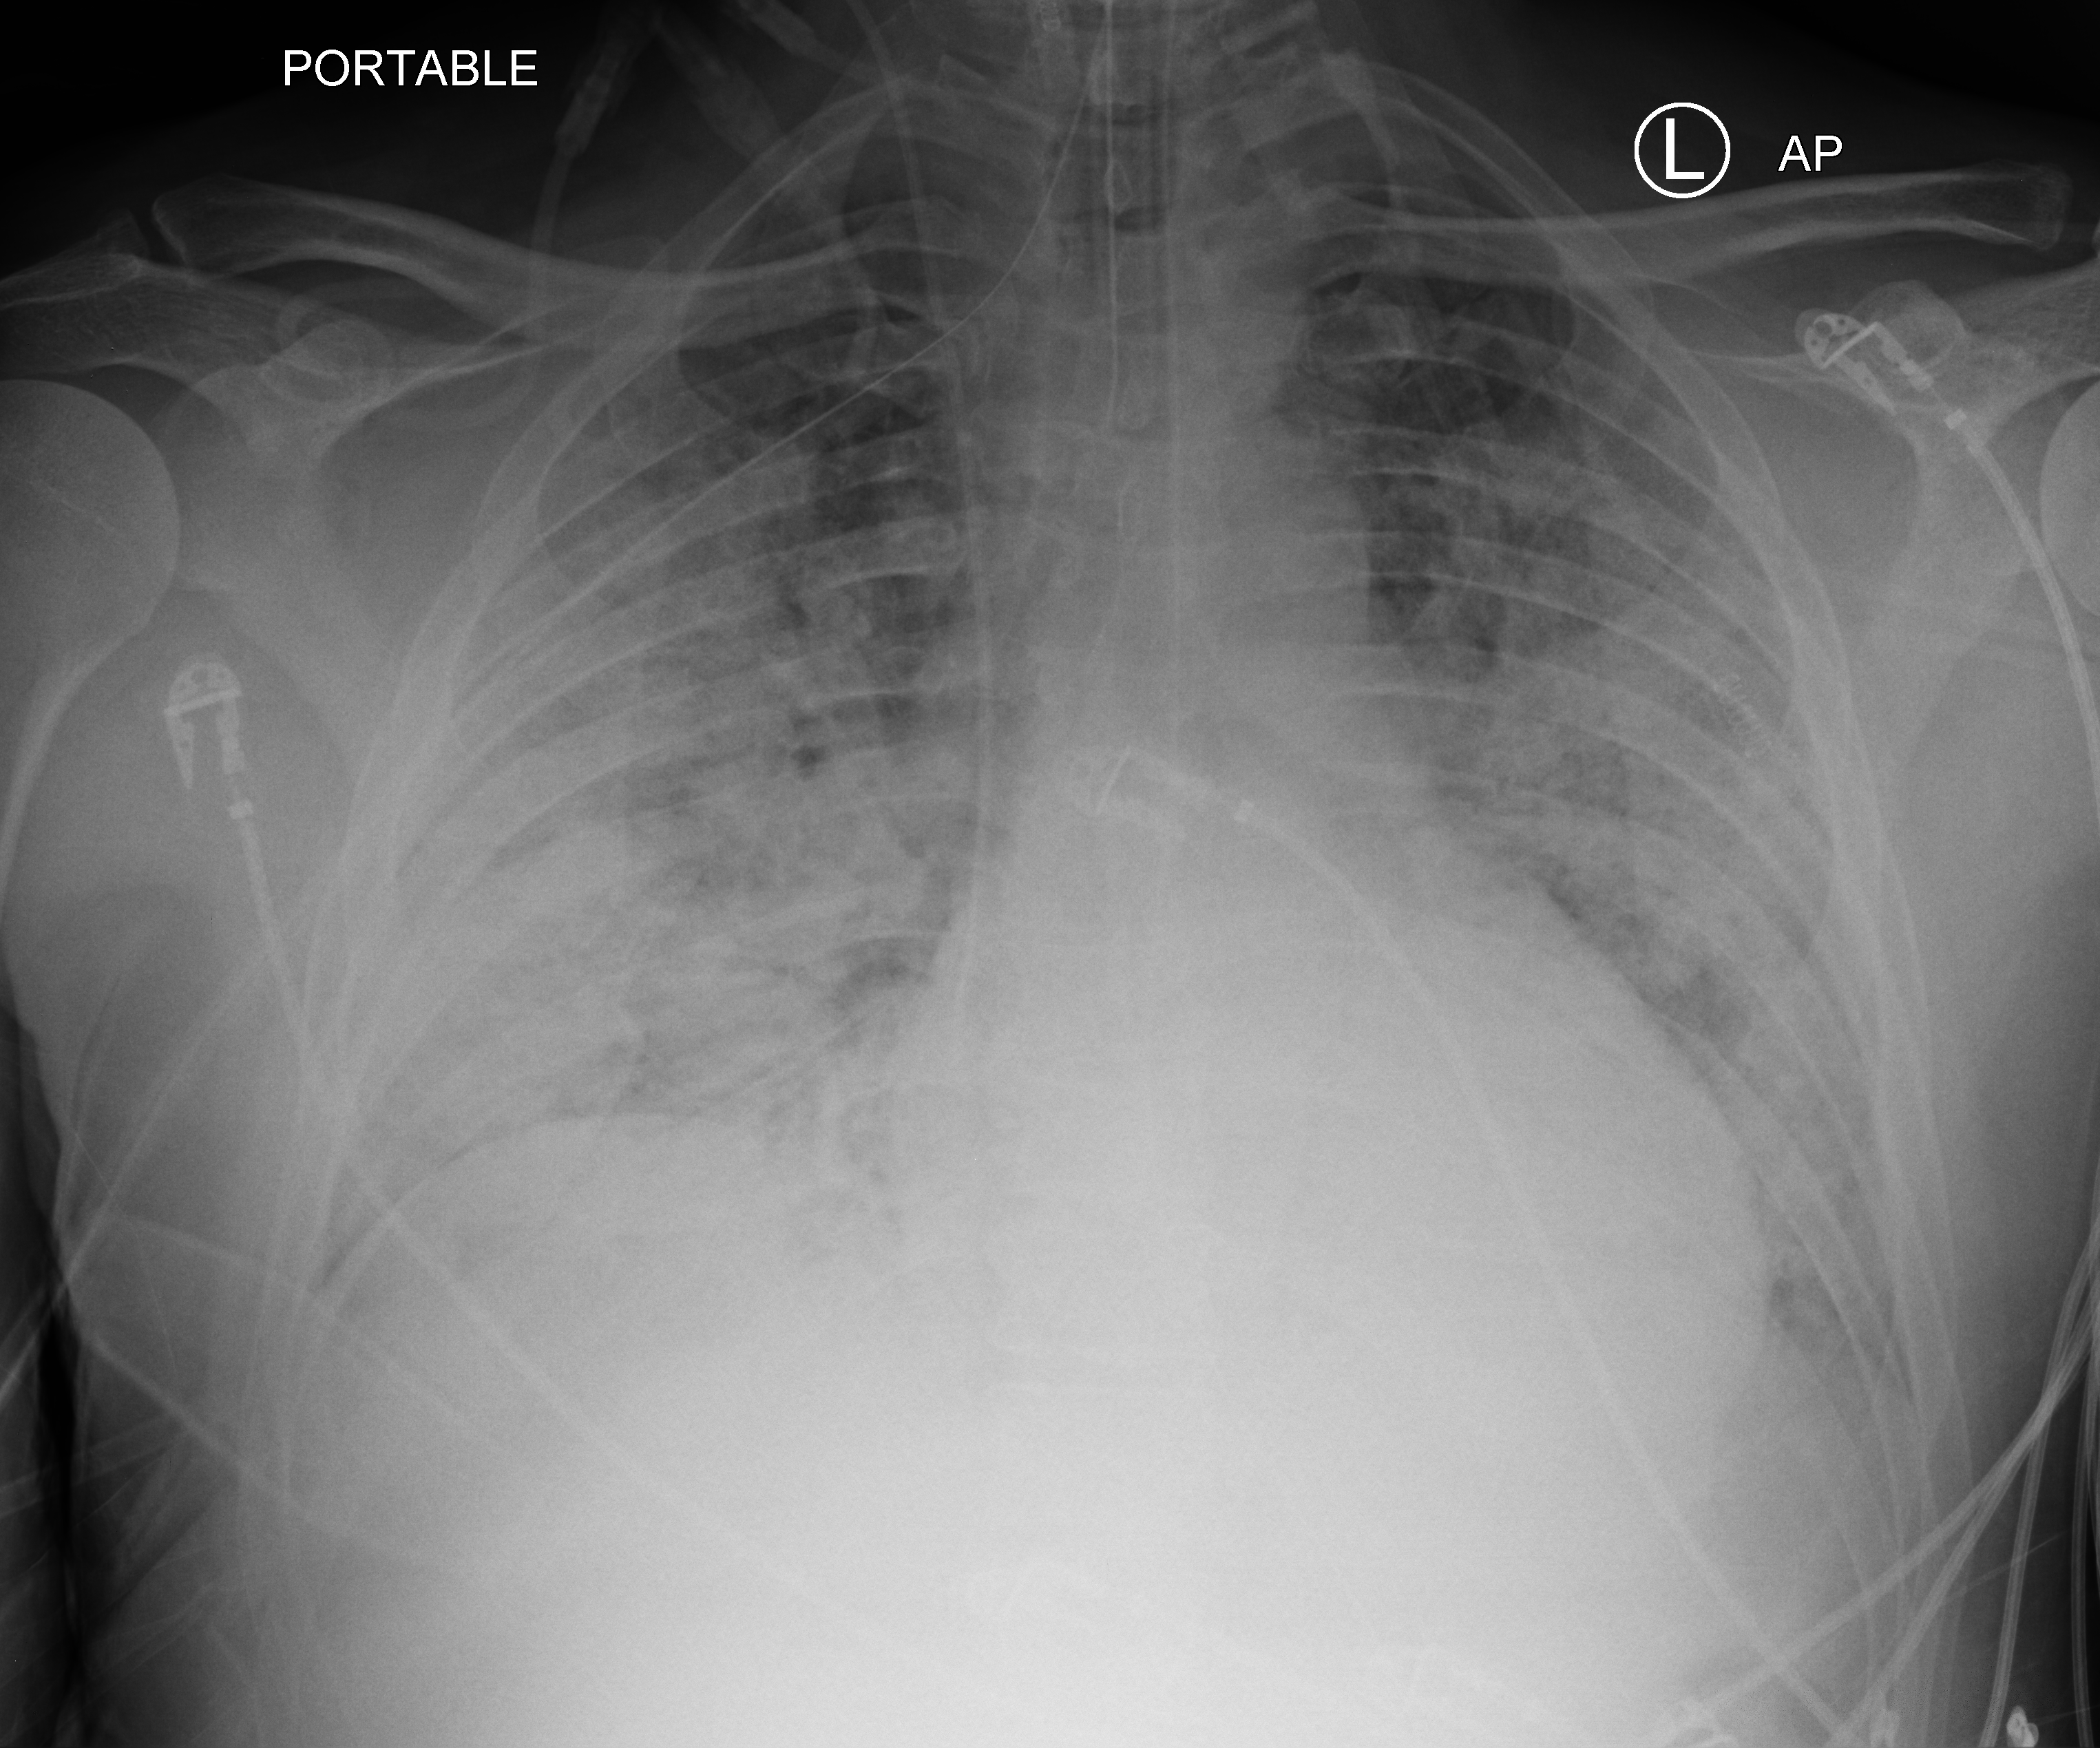
Portable chest radiograph; anteroposterior (AP) projection. Patient hospitalised with COVID-19; male, aged 18–59 years.
From the hospital-stay record, not from the radiograph (when in the stay this image was taken is not recorded):
- admitted to intensive care during this hospital stay: yes